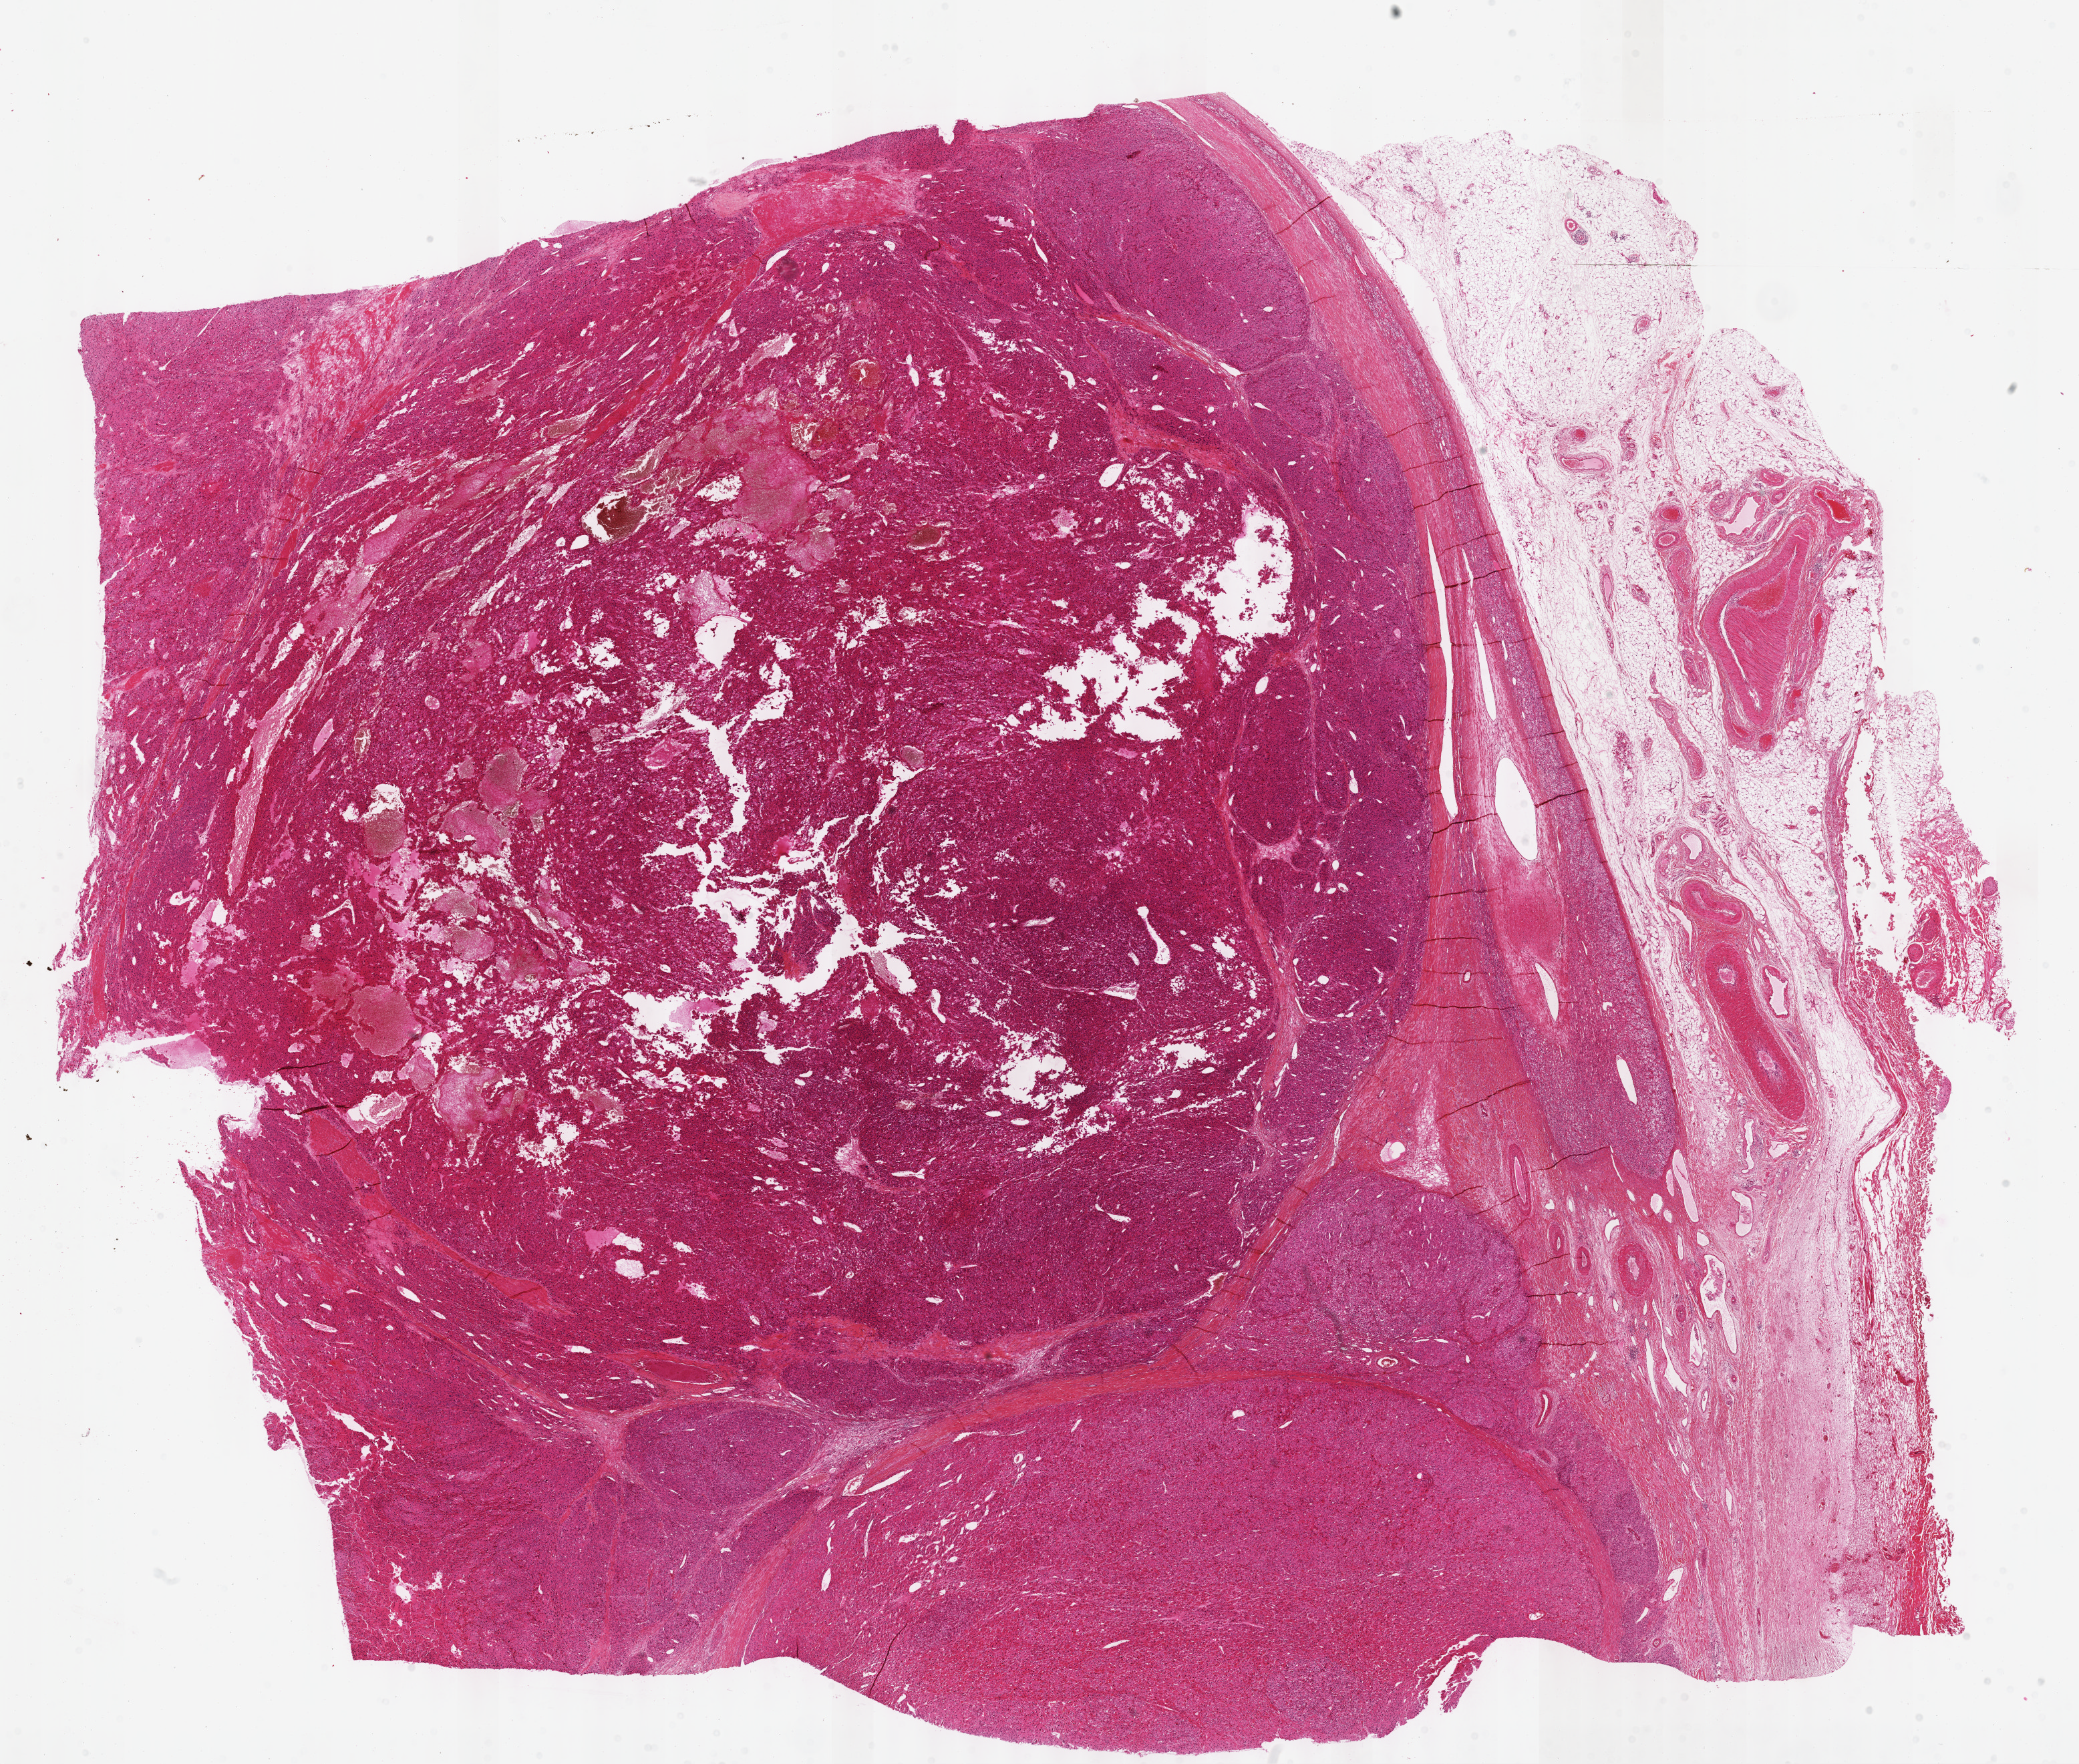
Hematoxylin and eosin (H&E) stained whole-slide image — a low-resolution overview of the entire scanned area, about 25.1 x 21.3 mm (acquisition: 40x scan); formalin-fixed paraffin-embedded (FFPE) diagnostic section; primary tumour sample from the adrenal cortex. Male, age 23 years at initial diagnosis.
Lymph nodes positive (case pathology): 0 of 32 examined. Pathologic diagnosis: Adrenal cortical carcinoma (cortex of adrenal gland).